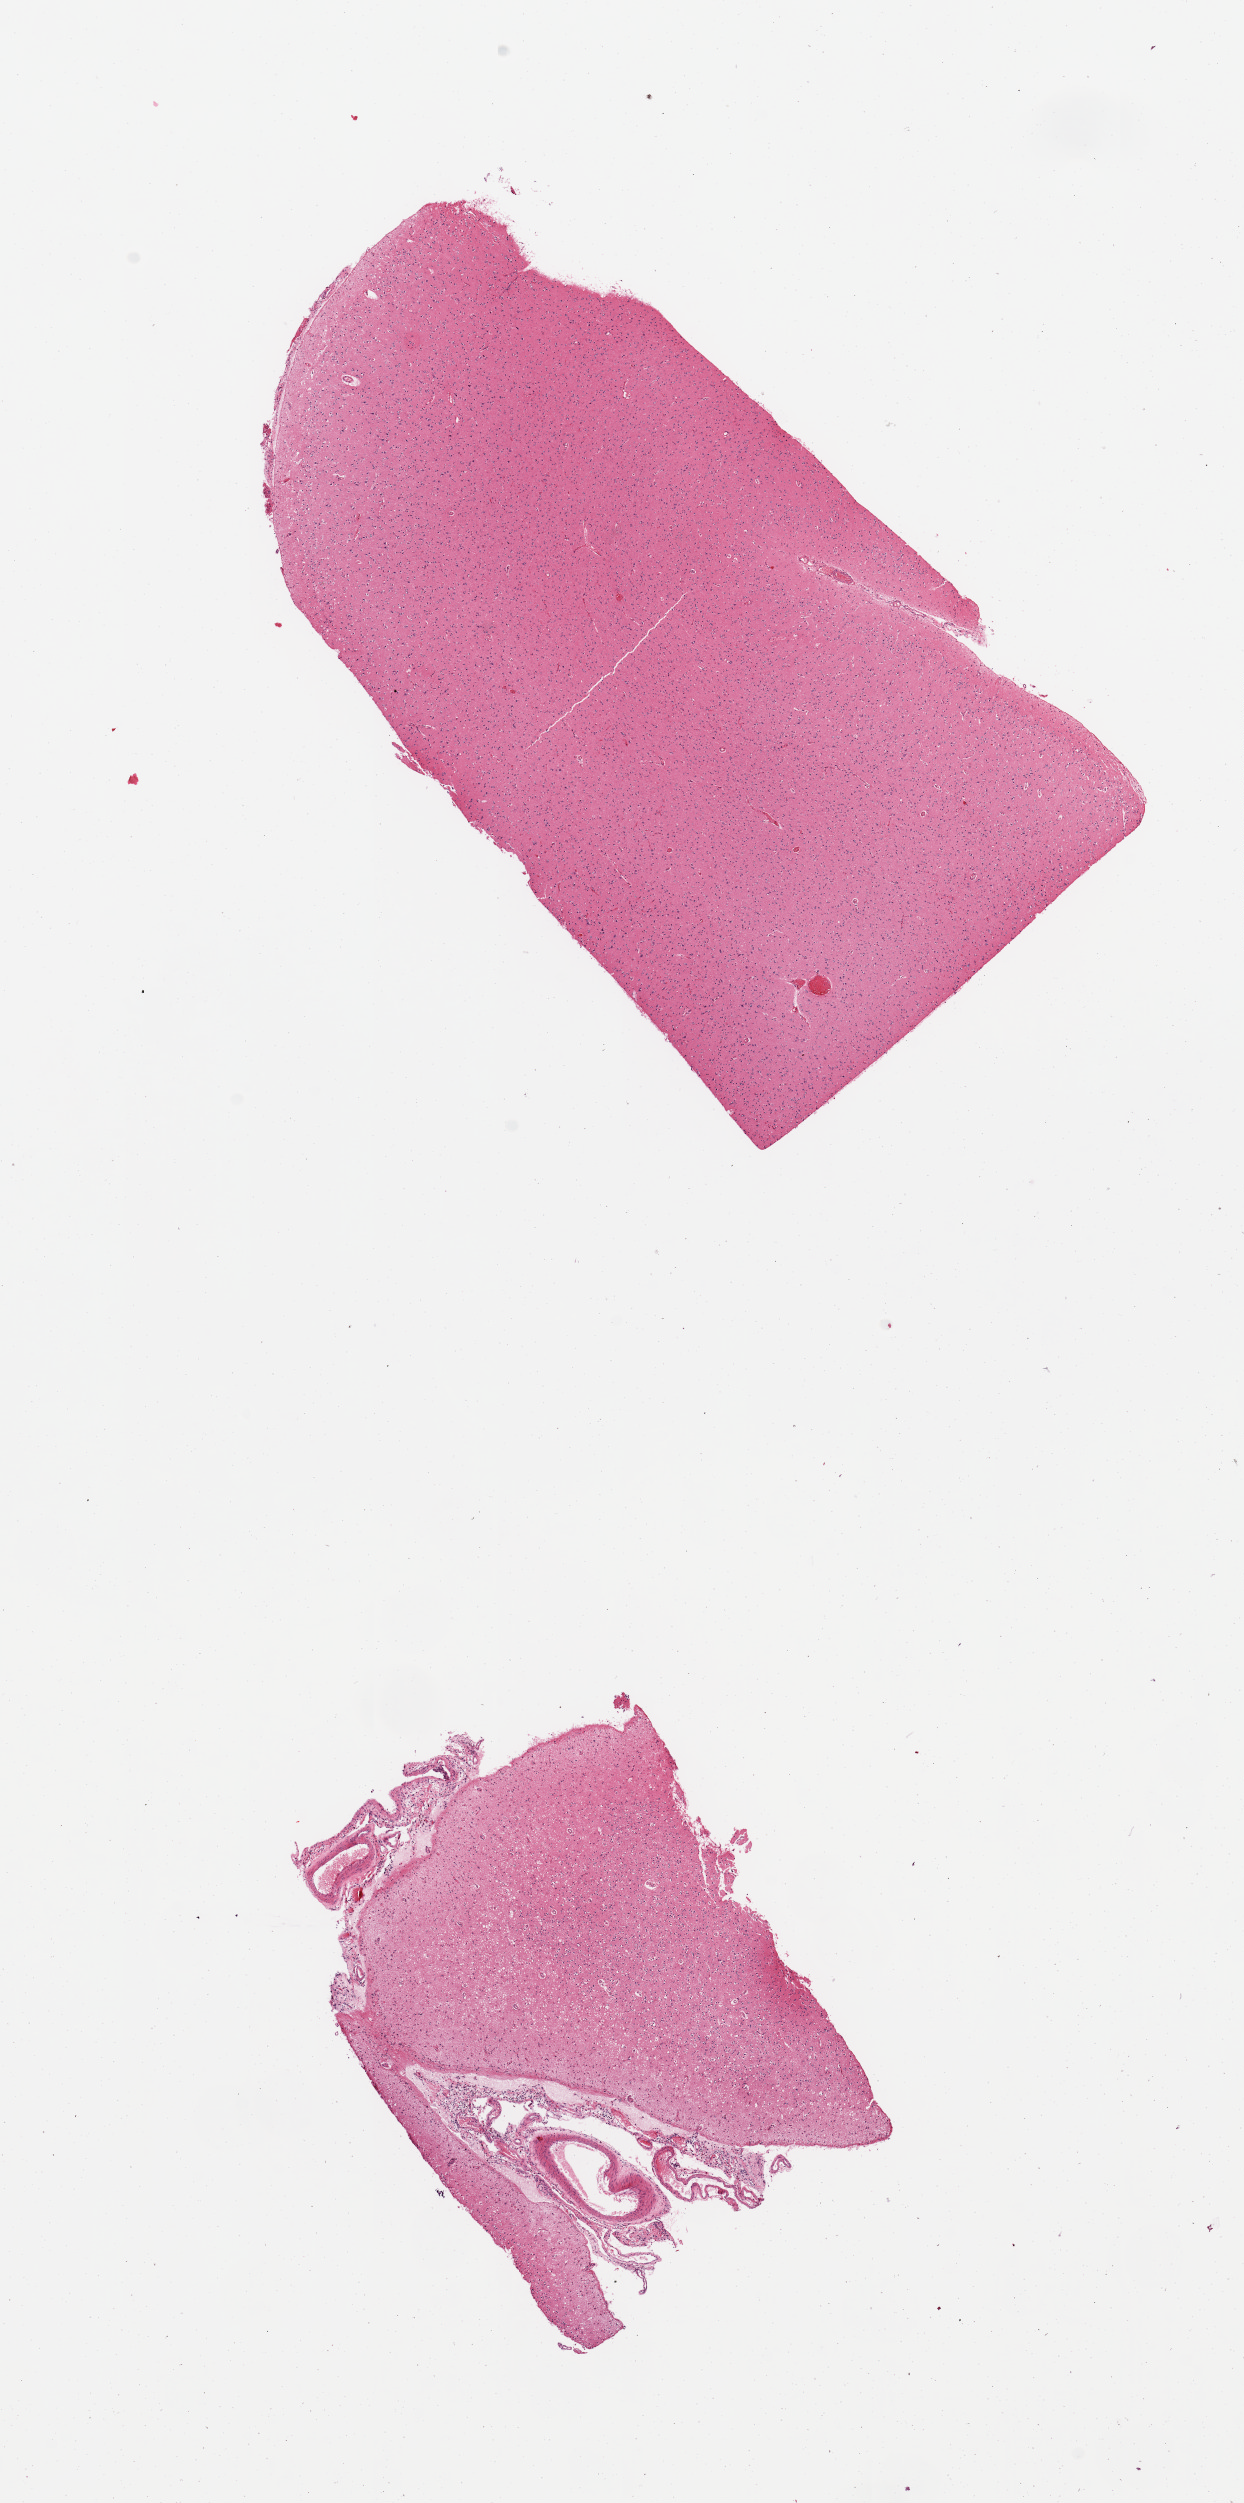
Digitized hematoxylin and eosin (H&E)-stained section — a low-resolution overview of the entire scanned area, about 9.8 x 19.8 mm (from a 20x scan); PAXgene-fixed paraffin-embedded (PFPE) section; target tissue: cerebral cortex; donor tissue sample. Donor: male.
Reviewer comment on this tissue sample: 2 pieces; meninges comprise 40% of smaller piece.